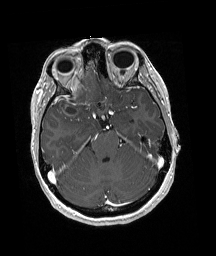
Brain MRI from a brain-tumour surgery series, one axial slice. Position 125 of 192 along the scan axis. T1-weighted post-contrast. 216 × 256 image matrix, field of view 211 × 250 mm. Case-level facts recorded for this patient, not image findings: histopathology: Oligodendroglioma; WHO grade: 3; IDH mutation: yes; tumour location: Right Frontal.
Structures marked on this image (manually delineated by an expert):
- tumour: bounding box (x1, y1, x2, y2) in pixels: (53, 73, 97, 115)